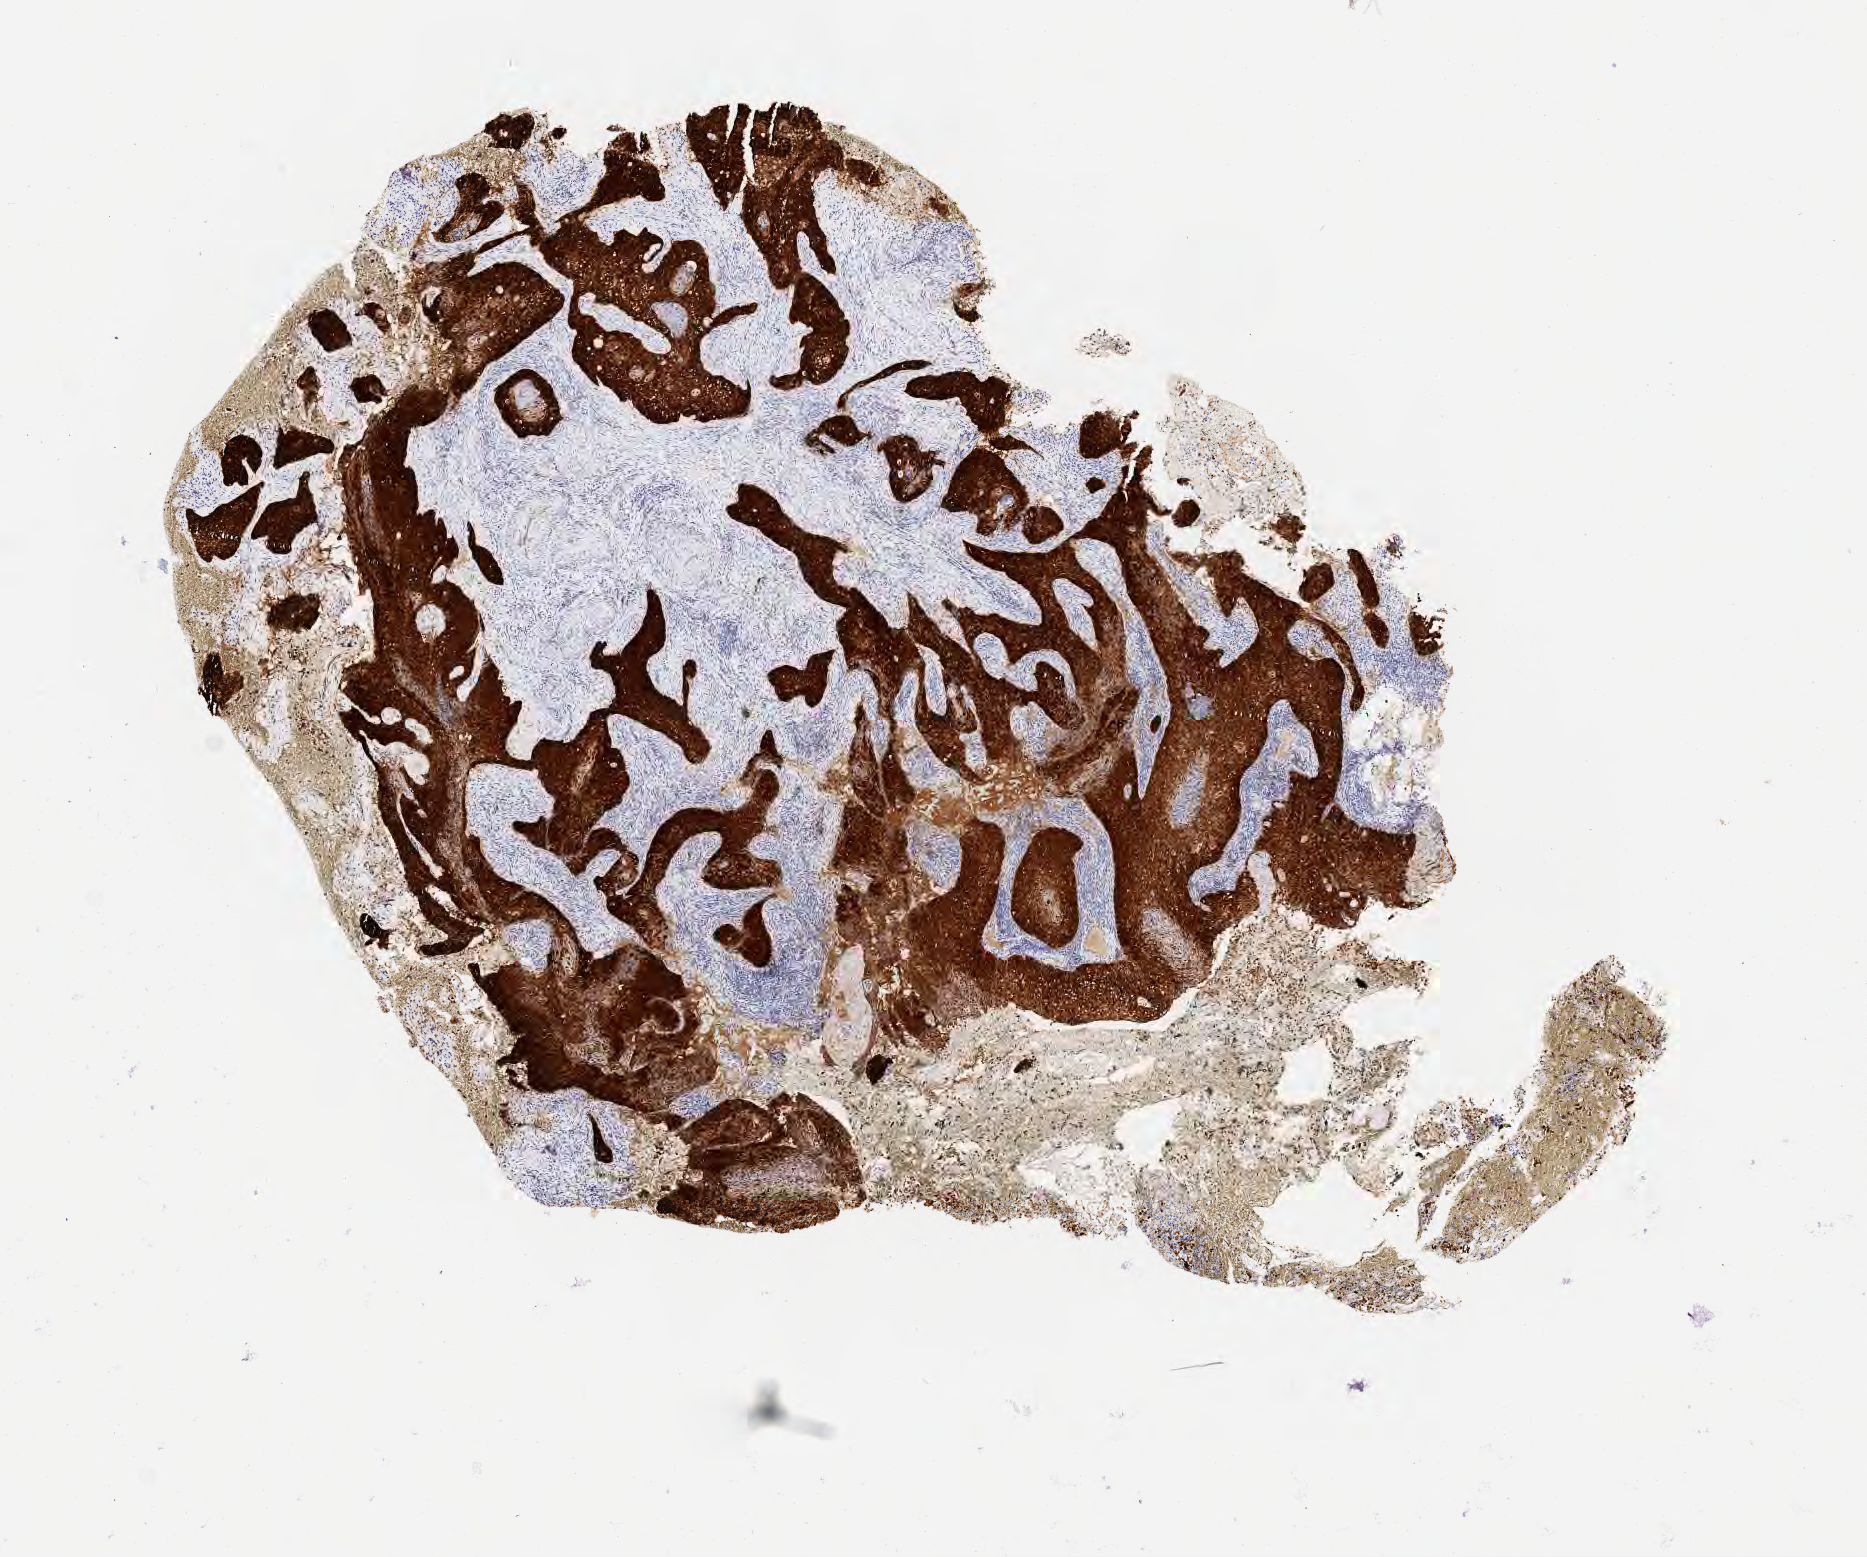
IHC for p16 (p16INK4a), whole-slide image — whole scanned area (about 7.6 x 6.3 mm) shown as a low-resolution overview; specimen: tumor tissue; site: cervix. Patient: female, aged 32.
Diagnosis: Squamous cell carcinoma, keratinizing, NOS.